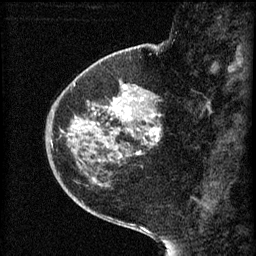
Breast MRI (dynamic contrast-enhanced), one sagittal slice. Position 20 of 60 along the scan axis. 3 images stored at this slice position (order not interpretable as contrast timing). 1.5 T. TE 4.2 ms, TR 8.2 ms. 2 mm slice thickness. 256 × 256 image matrix, field of view 180 × 180 mm. Female patient, age 44 years.
Annotated regions visible in this slice (semi-automatically segmented with operator editing):
- analysis volume of interest (the breast-tissue region the enhancement analysis was run in; not a lesion): bounding box (x1, y1, x2, y2) in pixels: (73, 82, 164, 165)
- tumour enhancement mask (voxels above the 70 % enhancement threshold inside the analysis volume of interest): (75, 84, 162, 159)